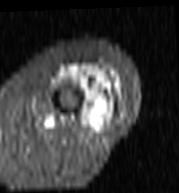
MRI of an extremity soft-tissue mass, one axial slice; position 37 of 103 along the scan axis; STIR; MR volume resampled by the dataset authors to the PET/CT grid (not the native acquisition matrix); 179 × 193 image matrix, field of view 175 × 188 mm. Female patient. From the clinical record (not read from this slice): histological type: undifferentiated – high grade; grade: high; site of the primary tumour: left thigh.
Annotated regions visible in this slice (expert contour drawn on MRI and transferred to this co-registered scan by the dataset authors):
- gross tumour volume including surrounding oedema: bounding box (x1, y1, x2, y2) in pixels: (59, 64, 122, 127)